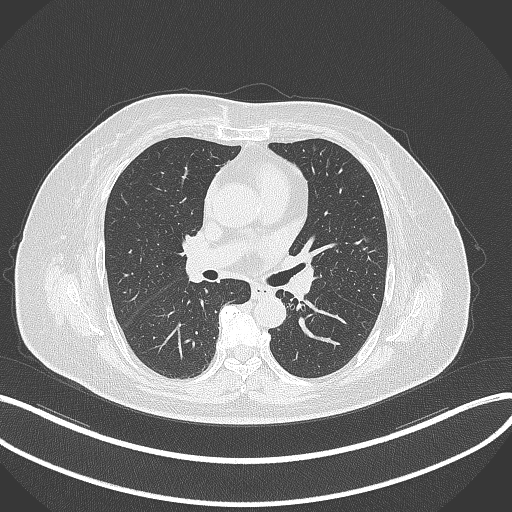
Chest CT, one axial slice. Position 201 of 315 along the scan axis. 120 kVp. Lung window (W 1500 / L -600 HU). 512 × 512 image matrix, field of view 400 × 400 mm. Female patient, age 76 years. Case-level facts recorded for this patient, not image findings: clinical TNM (as recorded): T1b N0 M0.
Outlined on this slice (rectangle marked by the reading radiologist):
- lung tumour (recorded histology: adenocarcinoma): bounding box [x1, y1, x2, y2] px = [352, 227, 381, 261]